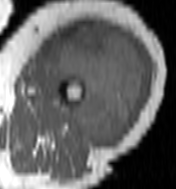
MRI of an extremity soft-tissue mass, one axial slice. Position 55 of 100 along the scan axis. MR volume resampled by the dataset authors to the PET/CT grid (not the native acquisition matrix). 3.27 mm slice thickness. 176 × 189 image matrix. Female patient. Case-level facts recorded for this patient, not image findings: histological type: undifferentiated – high grade; grade: high; site of the primary tumour: left thigh.
Structures marked on this image (expert contour drawn on MRI and transferred to this co-registered scan by the dataset authors):
- gross tumour volume including surrounding oedema: bounding box [x1, y1, x2, y2] px = [48, 25, 145, 147]
- gross tumour volume (mass): [48, 25, 145, 147]